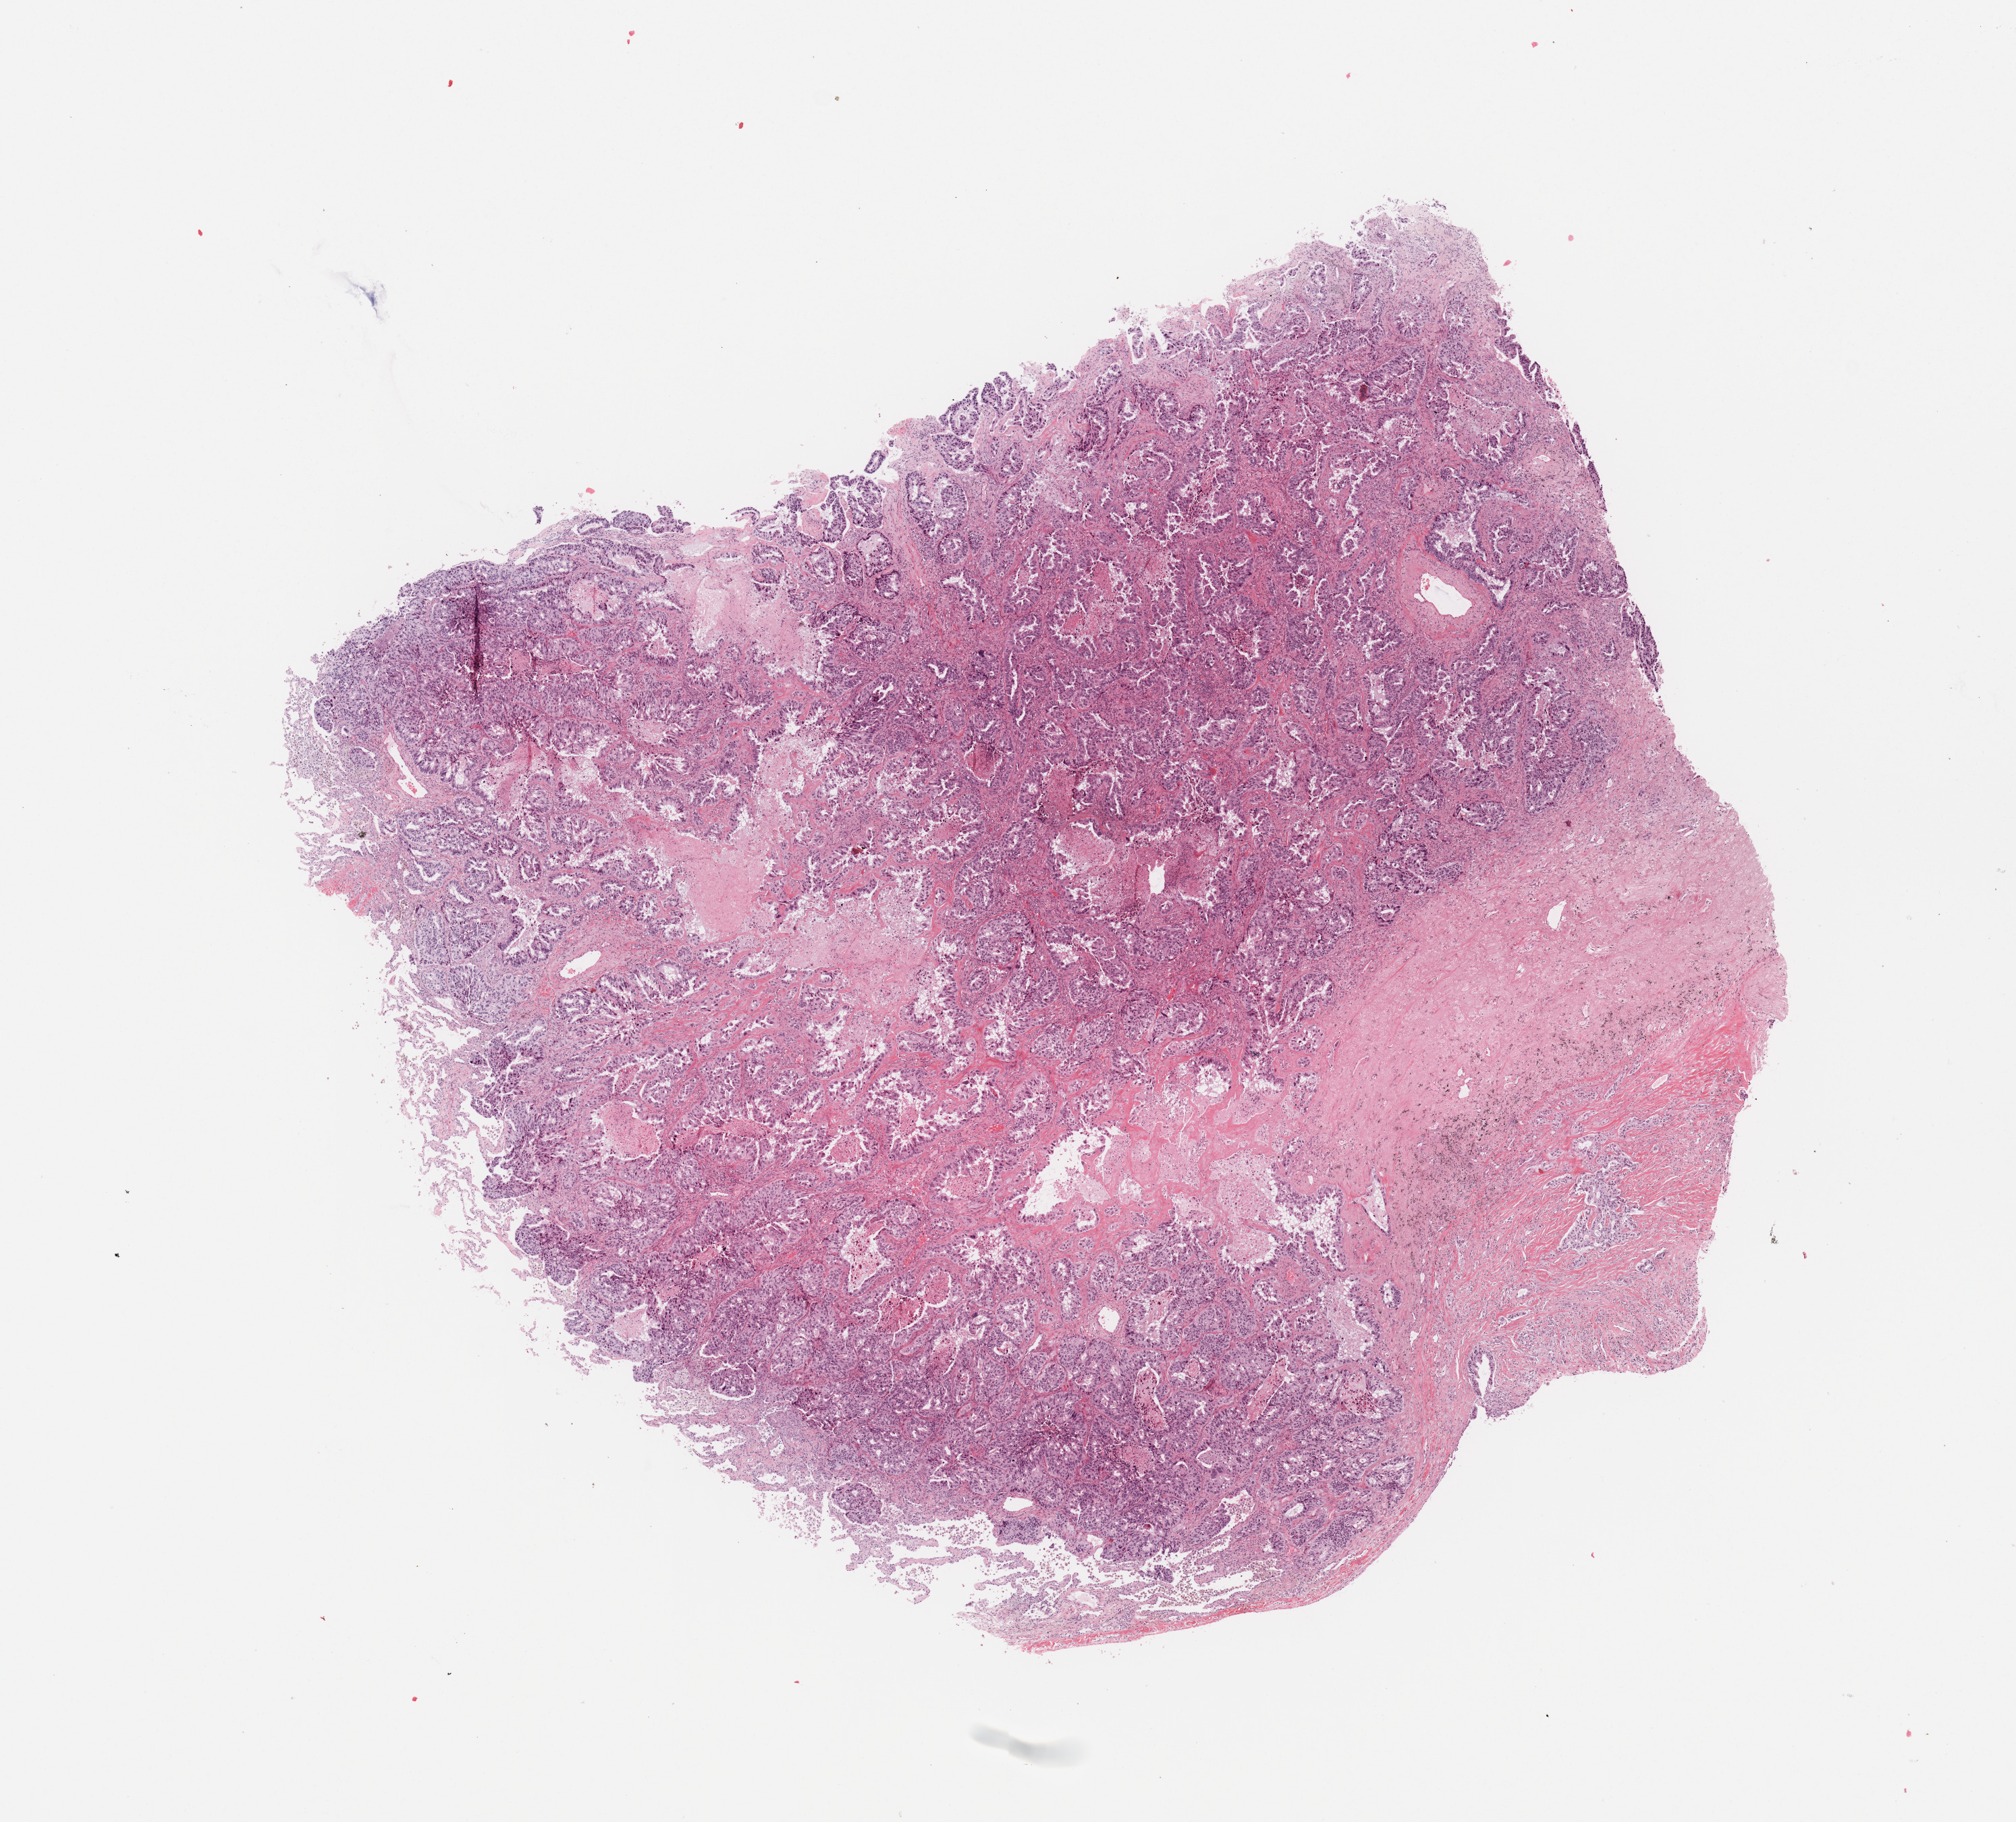
Whole-slide histology image, Hematoxylin and eosin (H&E) stained — a low-resolution overview of the entire scanned area, about 11.8 x 10.7 mm (acquisition: 20x scan); tumour tissue sample, sampled site: lung. Male, 62 y/o. Histologic grade: G2 (moderately differentiated). Composition of this section per pathologist review: tumour nuclei 70%, necrosis 5%.
AJCC pathologic stage: IIB. Diagnosis: Adenocarcinoma, NOS.